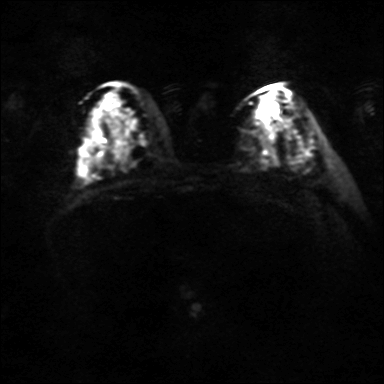
Breast MRI, one axial slice; position 20 of 36 along the scan axis; diffusion-weighted series; image 2 of 4 stored at this slice position (different b-values; order by instance number); 3 T; 4 mm slice thickness; 384 × 384 image matrix, field of view 320 × 320 mm. Female patient.
Outlined on this slice (manually delineated by an expert):
- tumour on diffusion-weighted imaging: bounding box (x1, y1, x2, y2) in pixels: (270, 115, 294, 129)